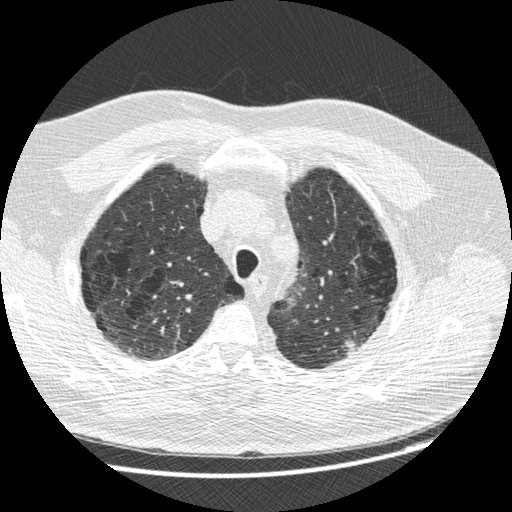
Low-dose screening chest CT, one axial slice. Slice 208 of 258 in the series (ordered by position). Reconstruction kernel STANDARD. 120 kVp. Lung window (W 1500 / L -600 HU). 1.25 mm slice thickness. 512 × 512 image matrix, field of view 370 × 370 mm.
Structures marked on this image (outlined manually by an expert reader):
- lesion 1 (tumor, upper lobe of left lung): box from (x=345, y=340) to (x=356, y=354) px